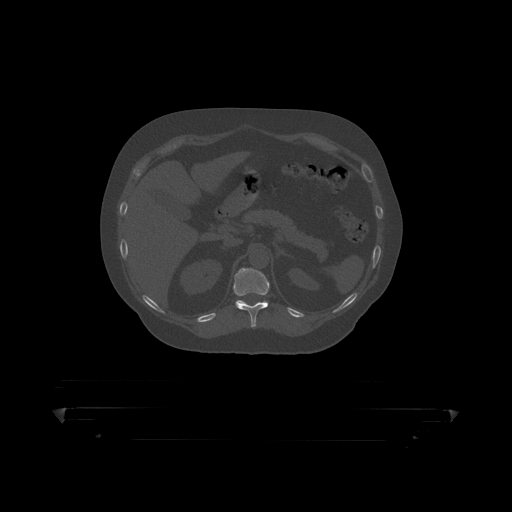
CT including the spine, one axial slice. Slice 190 of 390 in the series (ordered by position). Reconstruction kernel STANDARD. Bone window (W 1800 / L 400 HU). 1.25 mm slice thickness. 512 × 512 image matrix. Patient: male, 60 years. From the clinical record (not read from this slice): primary cancer: prostate.
Structures marked on this image (semi-automatic segmentation, software-assisted and operator-edited):
- T11 vertebra: box from (x=233, y=268) to (x=291, y=319) px
- T12 vertebra: (x=237, y=301)–(x=243, y=303)